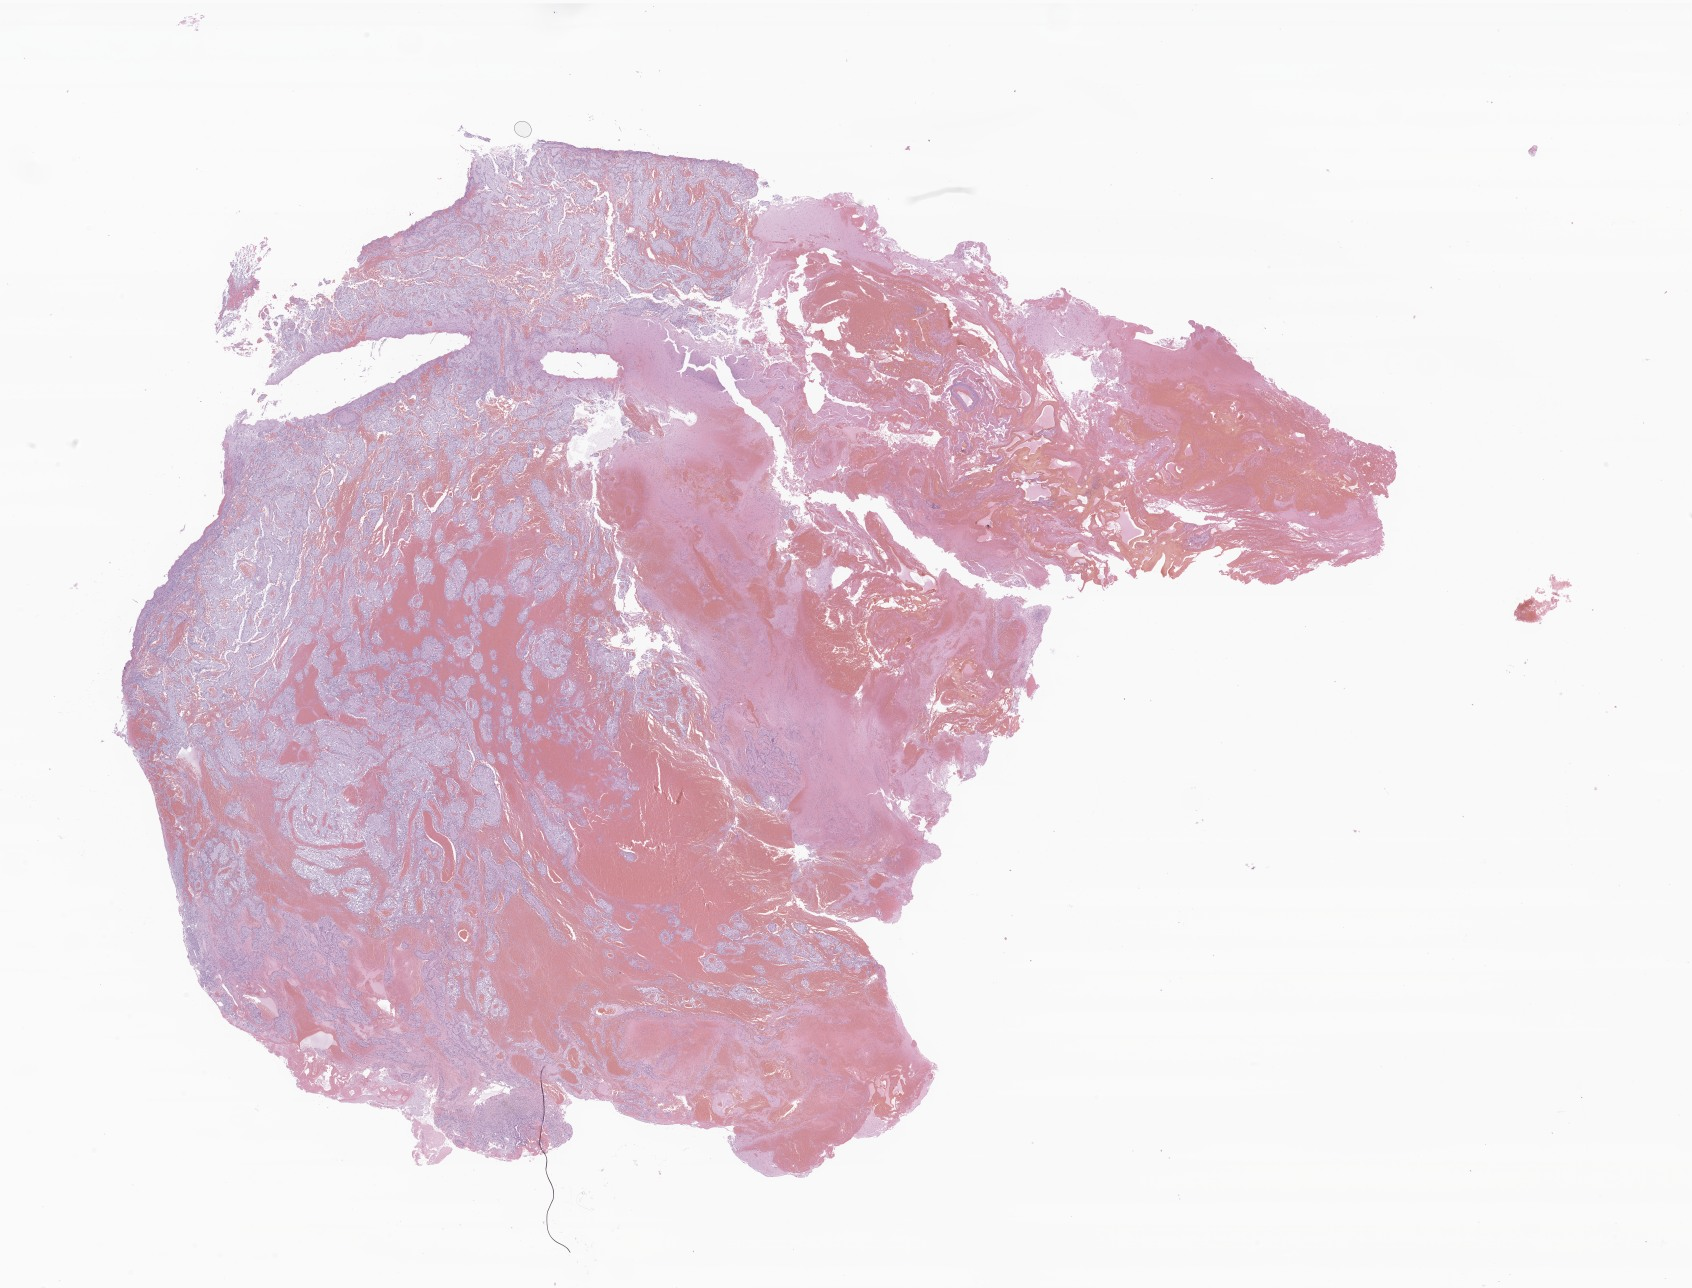
Whole-slide image, hematoxylin and eosin (H&E) stain of tumor tissue from the brain, a low-resolution overview of the entire scanned area, about 28.5 x 21.7 mm, FFPE section. Patient: male, age 65 months (5 years 5 months).
• recorded diagnosis: Neoplasm, malignant